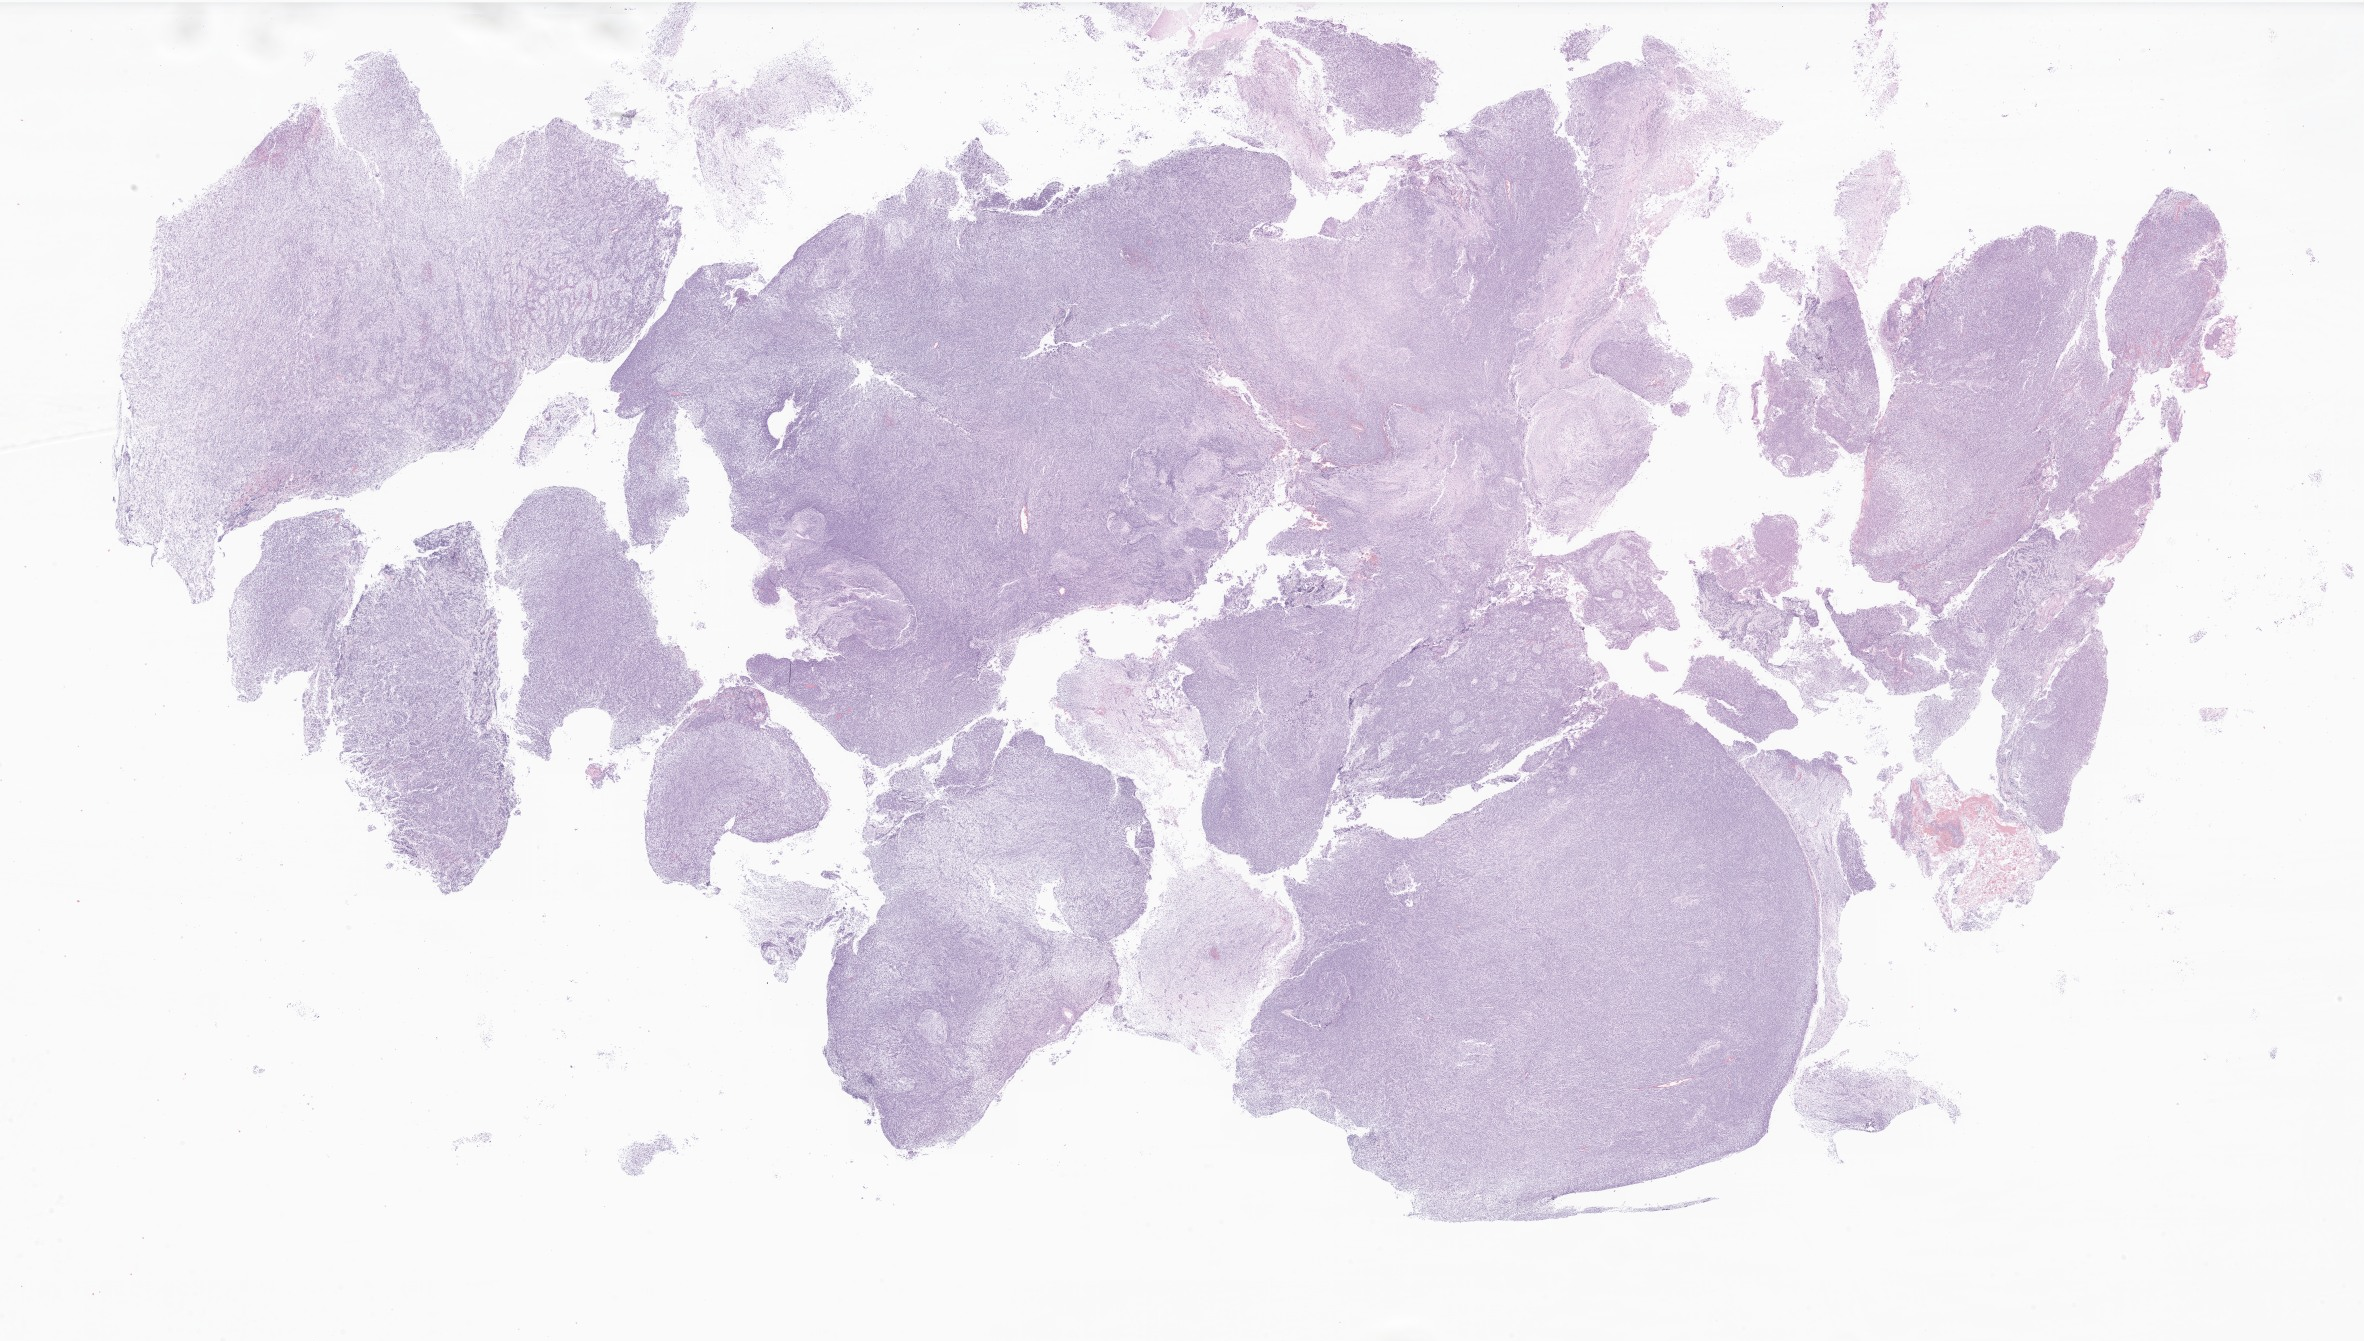
Whole-slide image, H&E stain of tumor tissue from the brain, whole scanned area (about 39.9 x 22.6 mm) shown as a low-resolution overview; FFPE section. Patient female; age 131 months (10 years 11 months).
* recorded diagnosis: Neoplasm, uncertain whether benign or malignant